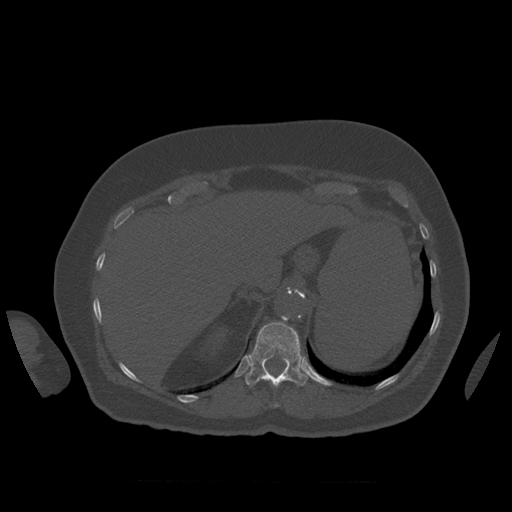
CT including the spine, one axial slice; position 304 of 399 along the scan axis; reconstruction kernel STANDARD; bone window (W 1800 / L 400 HU); 1.25 mm slice thickness; 512 × 512 image matrix, field of view 404 × 404 mm. Patient age 81 years. From the clinical record (not read from this slice): primary cancer: renal; vertebrae with lytic lesions (as recorded): L1.
Outlined on this slice (semi-automatic segmentation, software-assisted and operator-edited):
- T11 vertebra: bounding box [x1, y1, x2, y2] px = [276, 405, 278, 407]
- T12 vertebra: [245, 322, 308, 387]